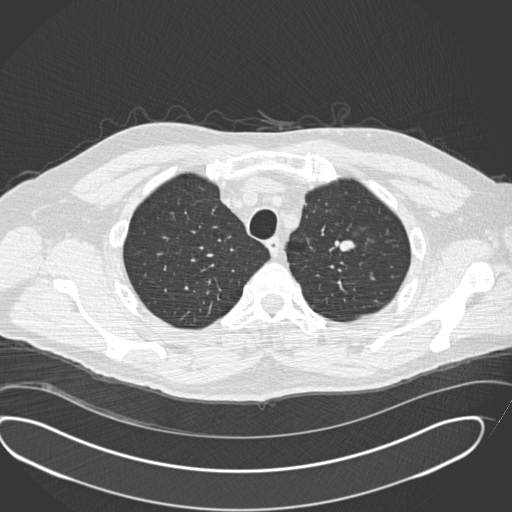
Low-dose screening chest CT, axial slice; second annual screen; lung window (W 1500 / L -600 HU); 2 mm slice thickness; standard (soft-tissue) reconstruction kernel (B30f); 120 kVp; slice 40 of 190 in the series. Male, age 56 years at enrolment. Current smoker at enrolment.
Expert reader's lesion annotation, bounding box (x1, y1, x2, y2) in pixels: (313, 228, 370, 271). Screening reader's record for this exam: no non-calcified nodule ≥4 mm recorded. Official screen result: negative screen, significant abnormalities not suspicious for lung cancer. Participant outcome: lung cancer diagnosed 520 days after this screen (after the third annual screen) — neuroendocrine carcinoma, NOS, left upper lobe, well differentiated (G1), stage IA (AJCC 6th edition), 20 mm at pathology.